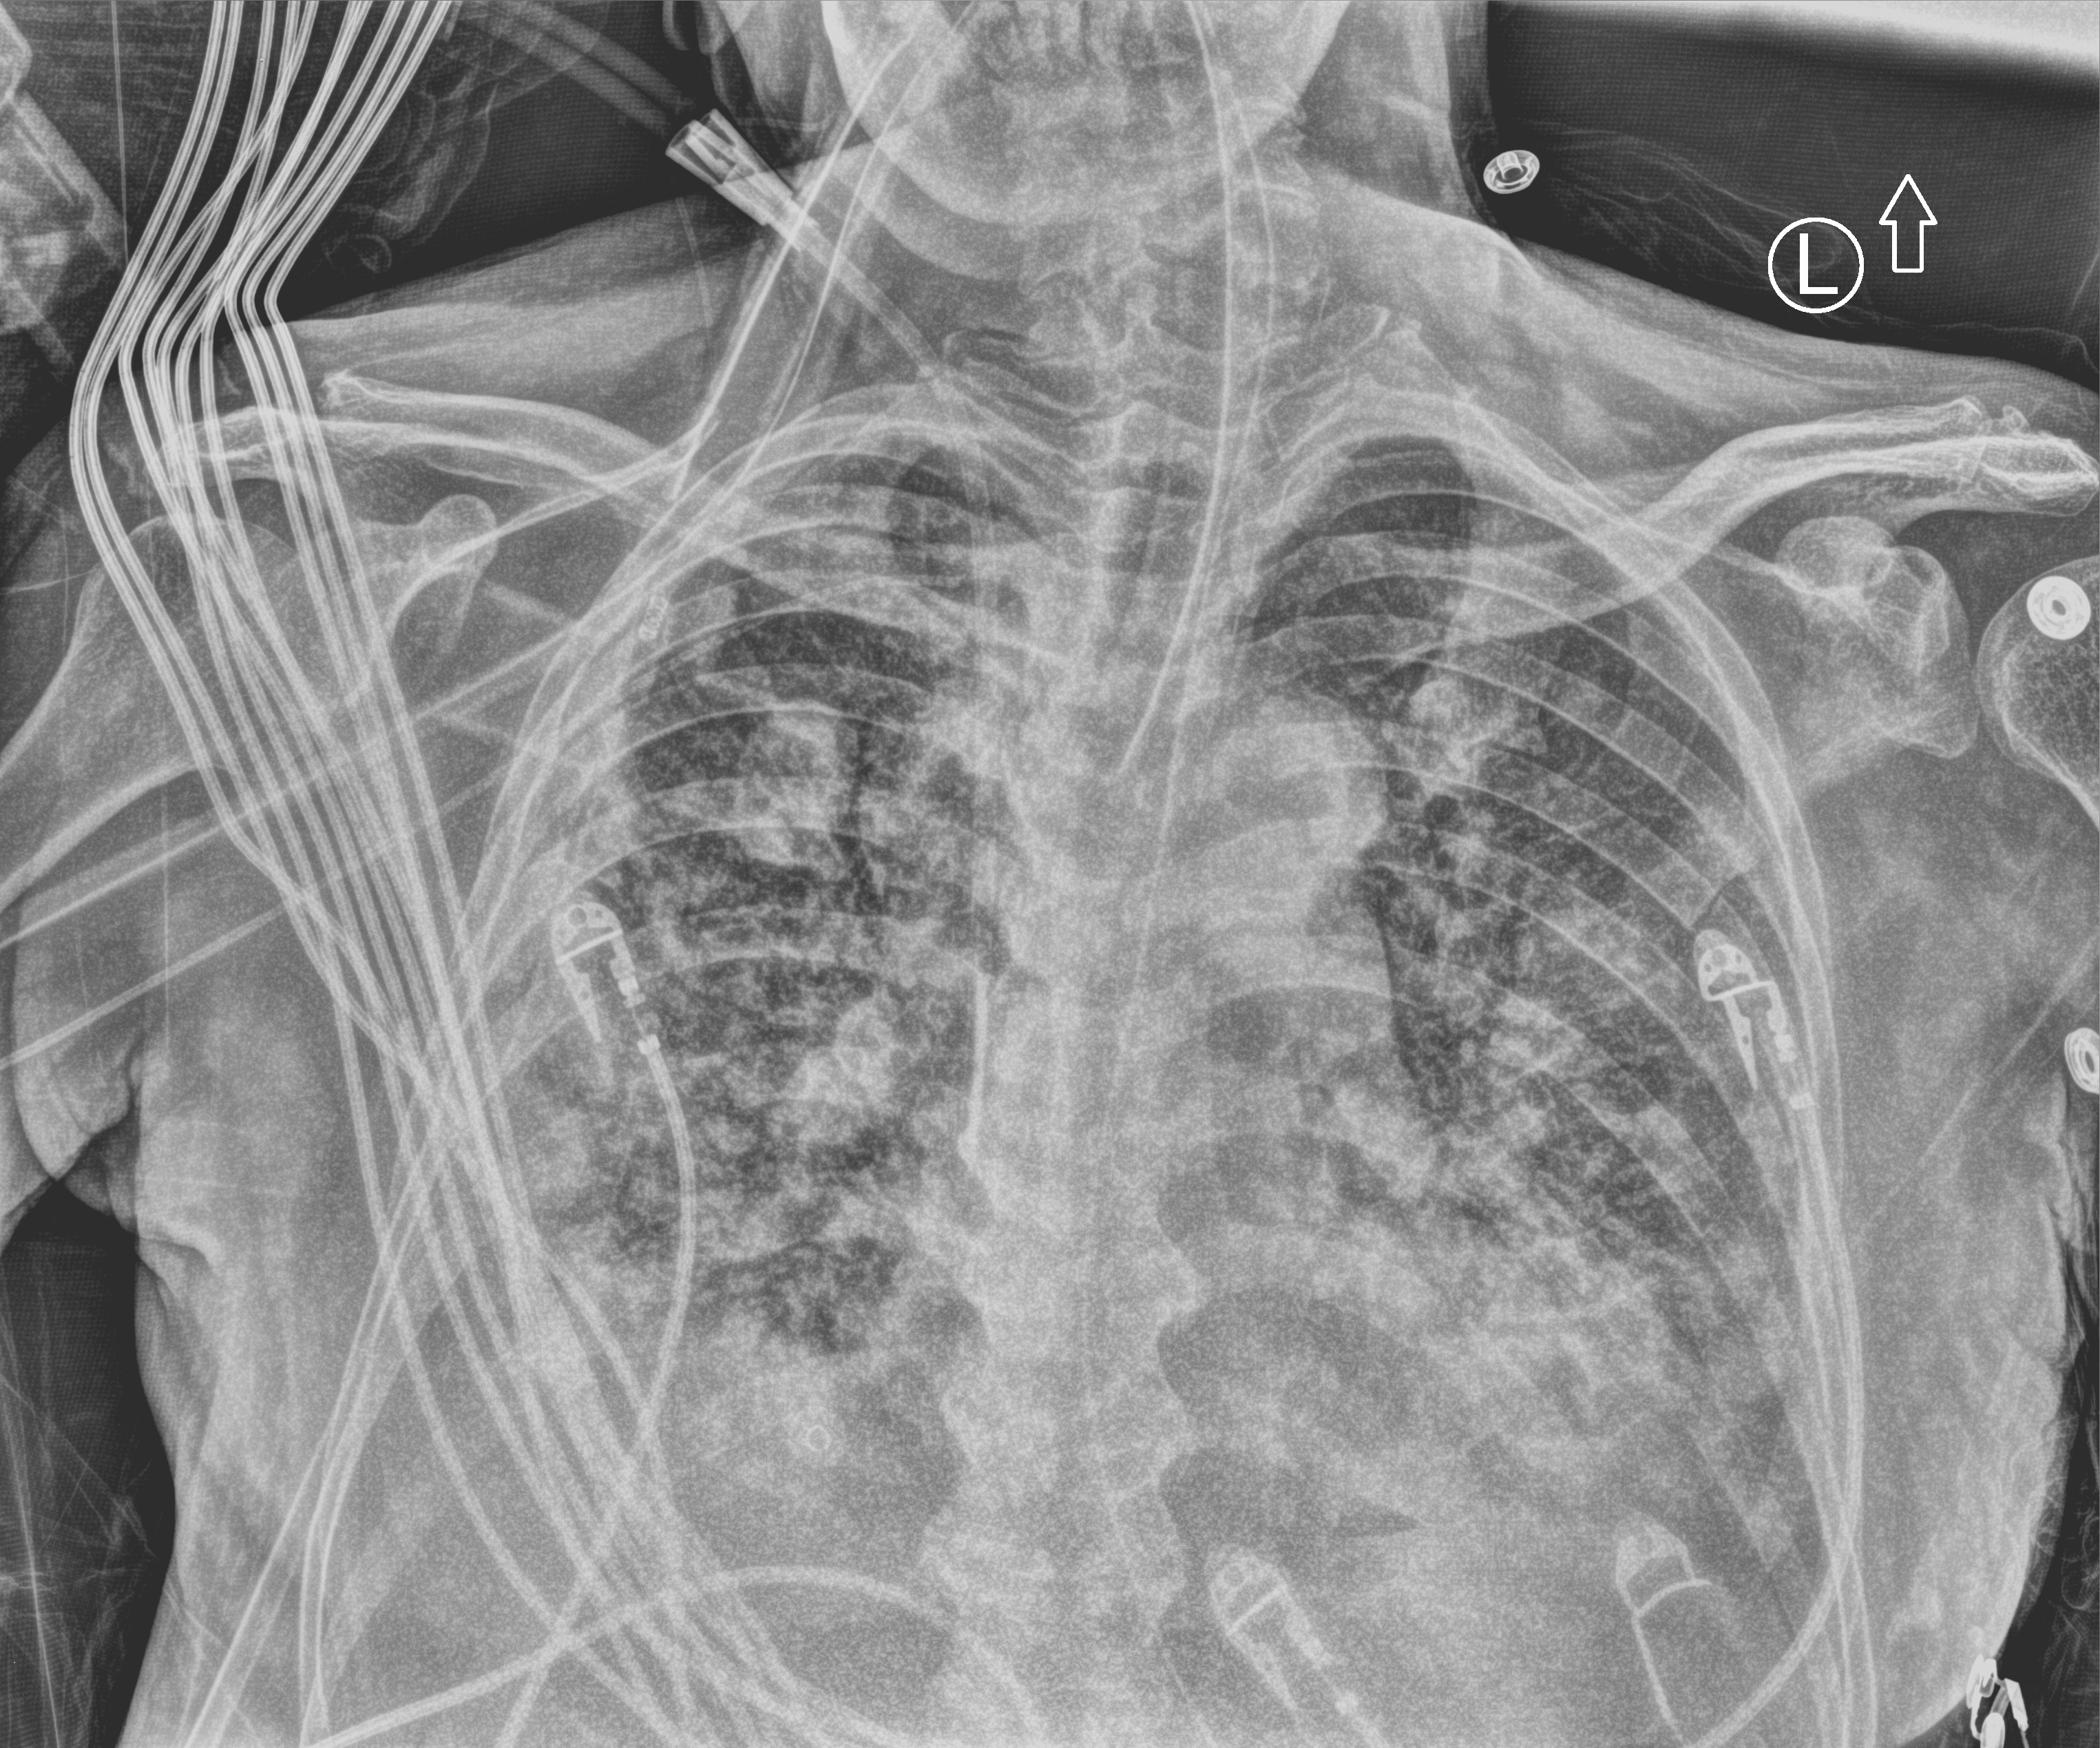
Portable chest radiograph; anteroposterior (AP) projection. Male patient hospitalised with COVID-19, age 60–74 years.
Hospital-stay facts (about this admission, not read from this image; timing relative to this image not recorded):
- chronic kidney disease (admission record): no
- smoking status (admission record): never